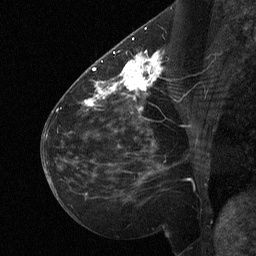
Breast MRI (dynamic contrast-enhanced), one sagittal slice; position 30 of 64 along the scan axis; dynamic contrast-enhanced study with each time point stored as its own series, time point 2 of 3 at this slice position (early post-contrast, ordered by acquisition time); 1.5 T; TE 4.8 ms, TR 27 ms; 2 mm slice thickness; 256 × 256 image matrix. Female patient, age 51 years. From the clinical record (not read from this slice): setting: breast cancer imaged before/during neoadjuvant chemotherapy; receptor status: HR-positive, HER2-negative.
Annotated regions visible in this slice (semi-automatic segmentation, software-assisted and operator-edited):
- analysis volume of interest (the breast-tissue region the enhancement analysis was run in; not a lesion): box from (x=112, y=46) to (x=169, y=106) px
- tumour enhancement mask (voxels above the 90 % enhancement threshold inside the analysis volume of interest): (x=112, y=54)–(x=159, y=100)